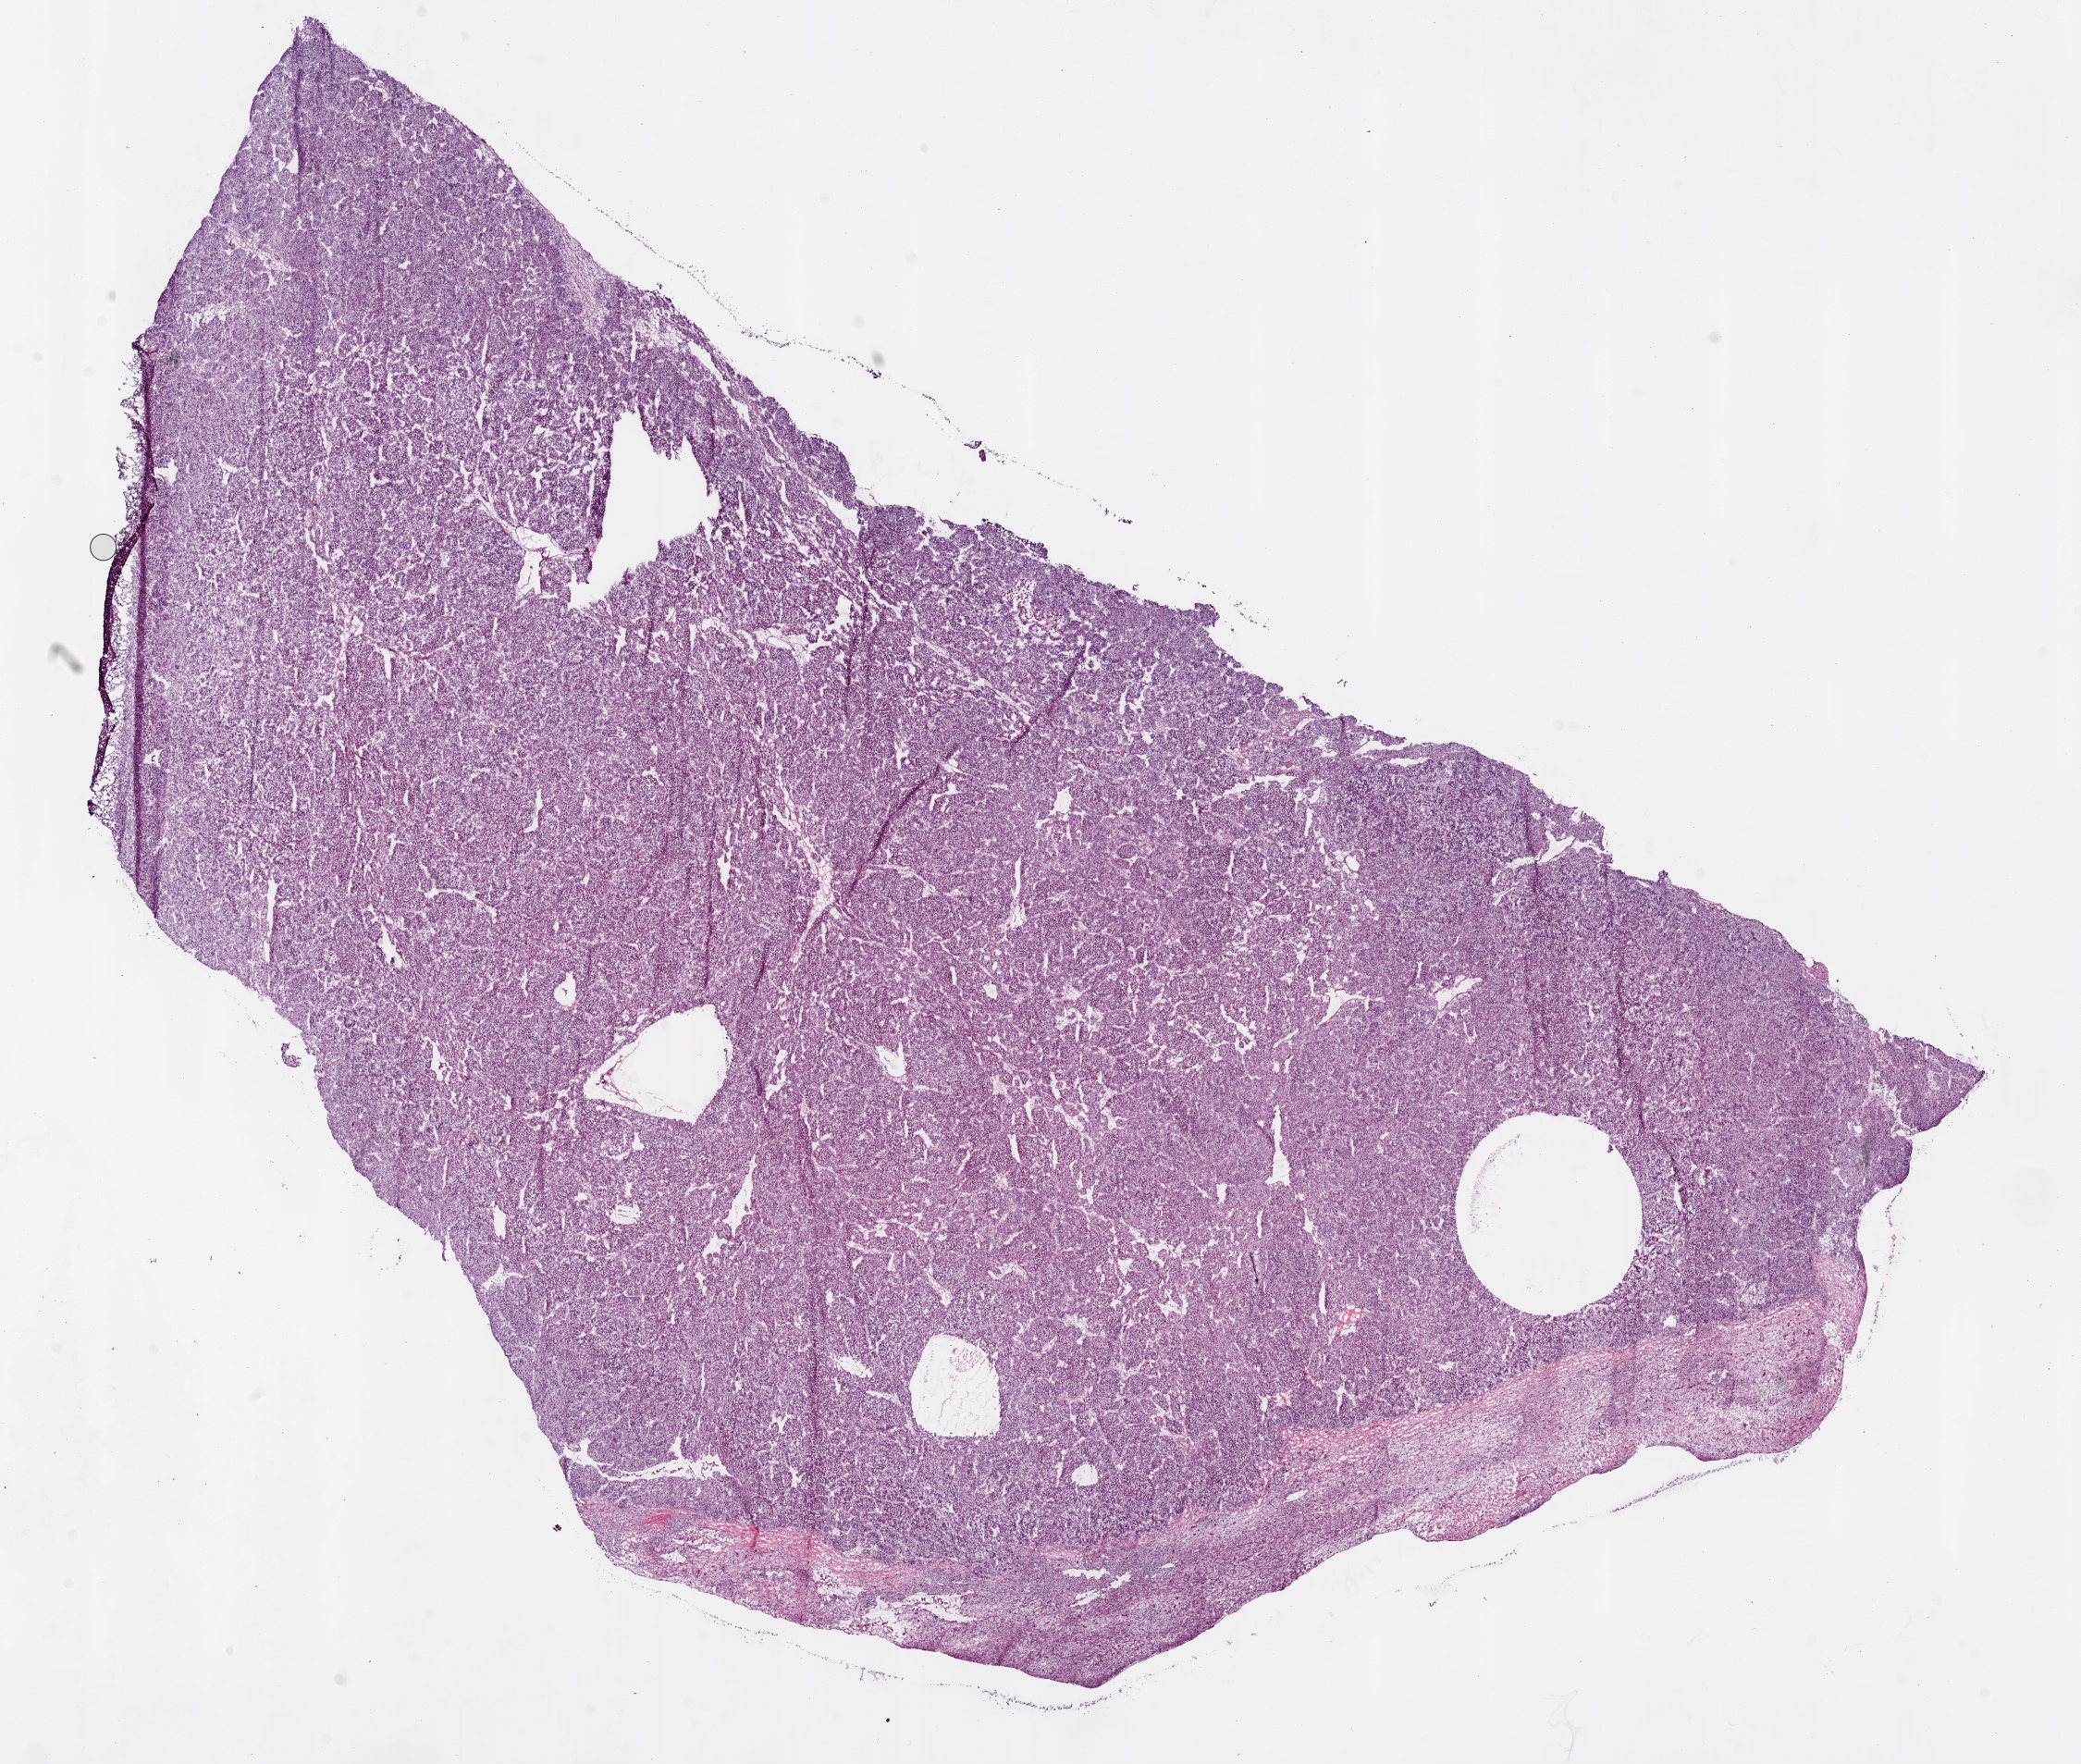
H&E-stained whole-slide image, a low-resolution overview of the entire scanned area, about 18.1 x 15.3 mm (acquisition: 20x scan). Frozen section from the bottom of the tissue portion. Liver, primary tumour sample. Male, age 48 years at initial diagnosis. Histologic grade: G2 (moderately differentiated). Slide review estimates, as recorded: tumour cells 90%, tumour nuclei 80%, normal cells 0%, stromal cells 10%, necrosis 0%.
• AJCC pathologic stage: II (6th edition)
• pathologic diagnosis: Hepatocellular carcinoma, NOS